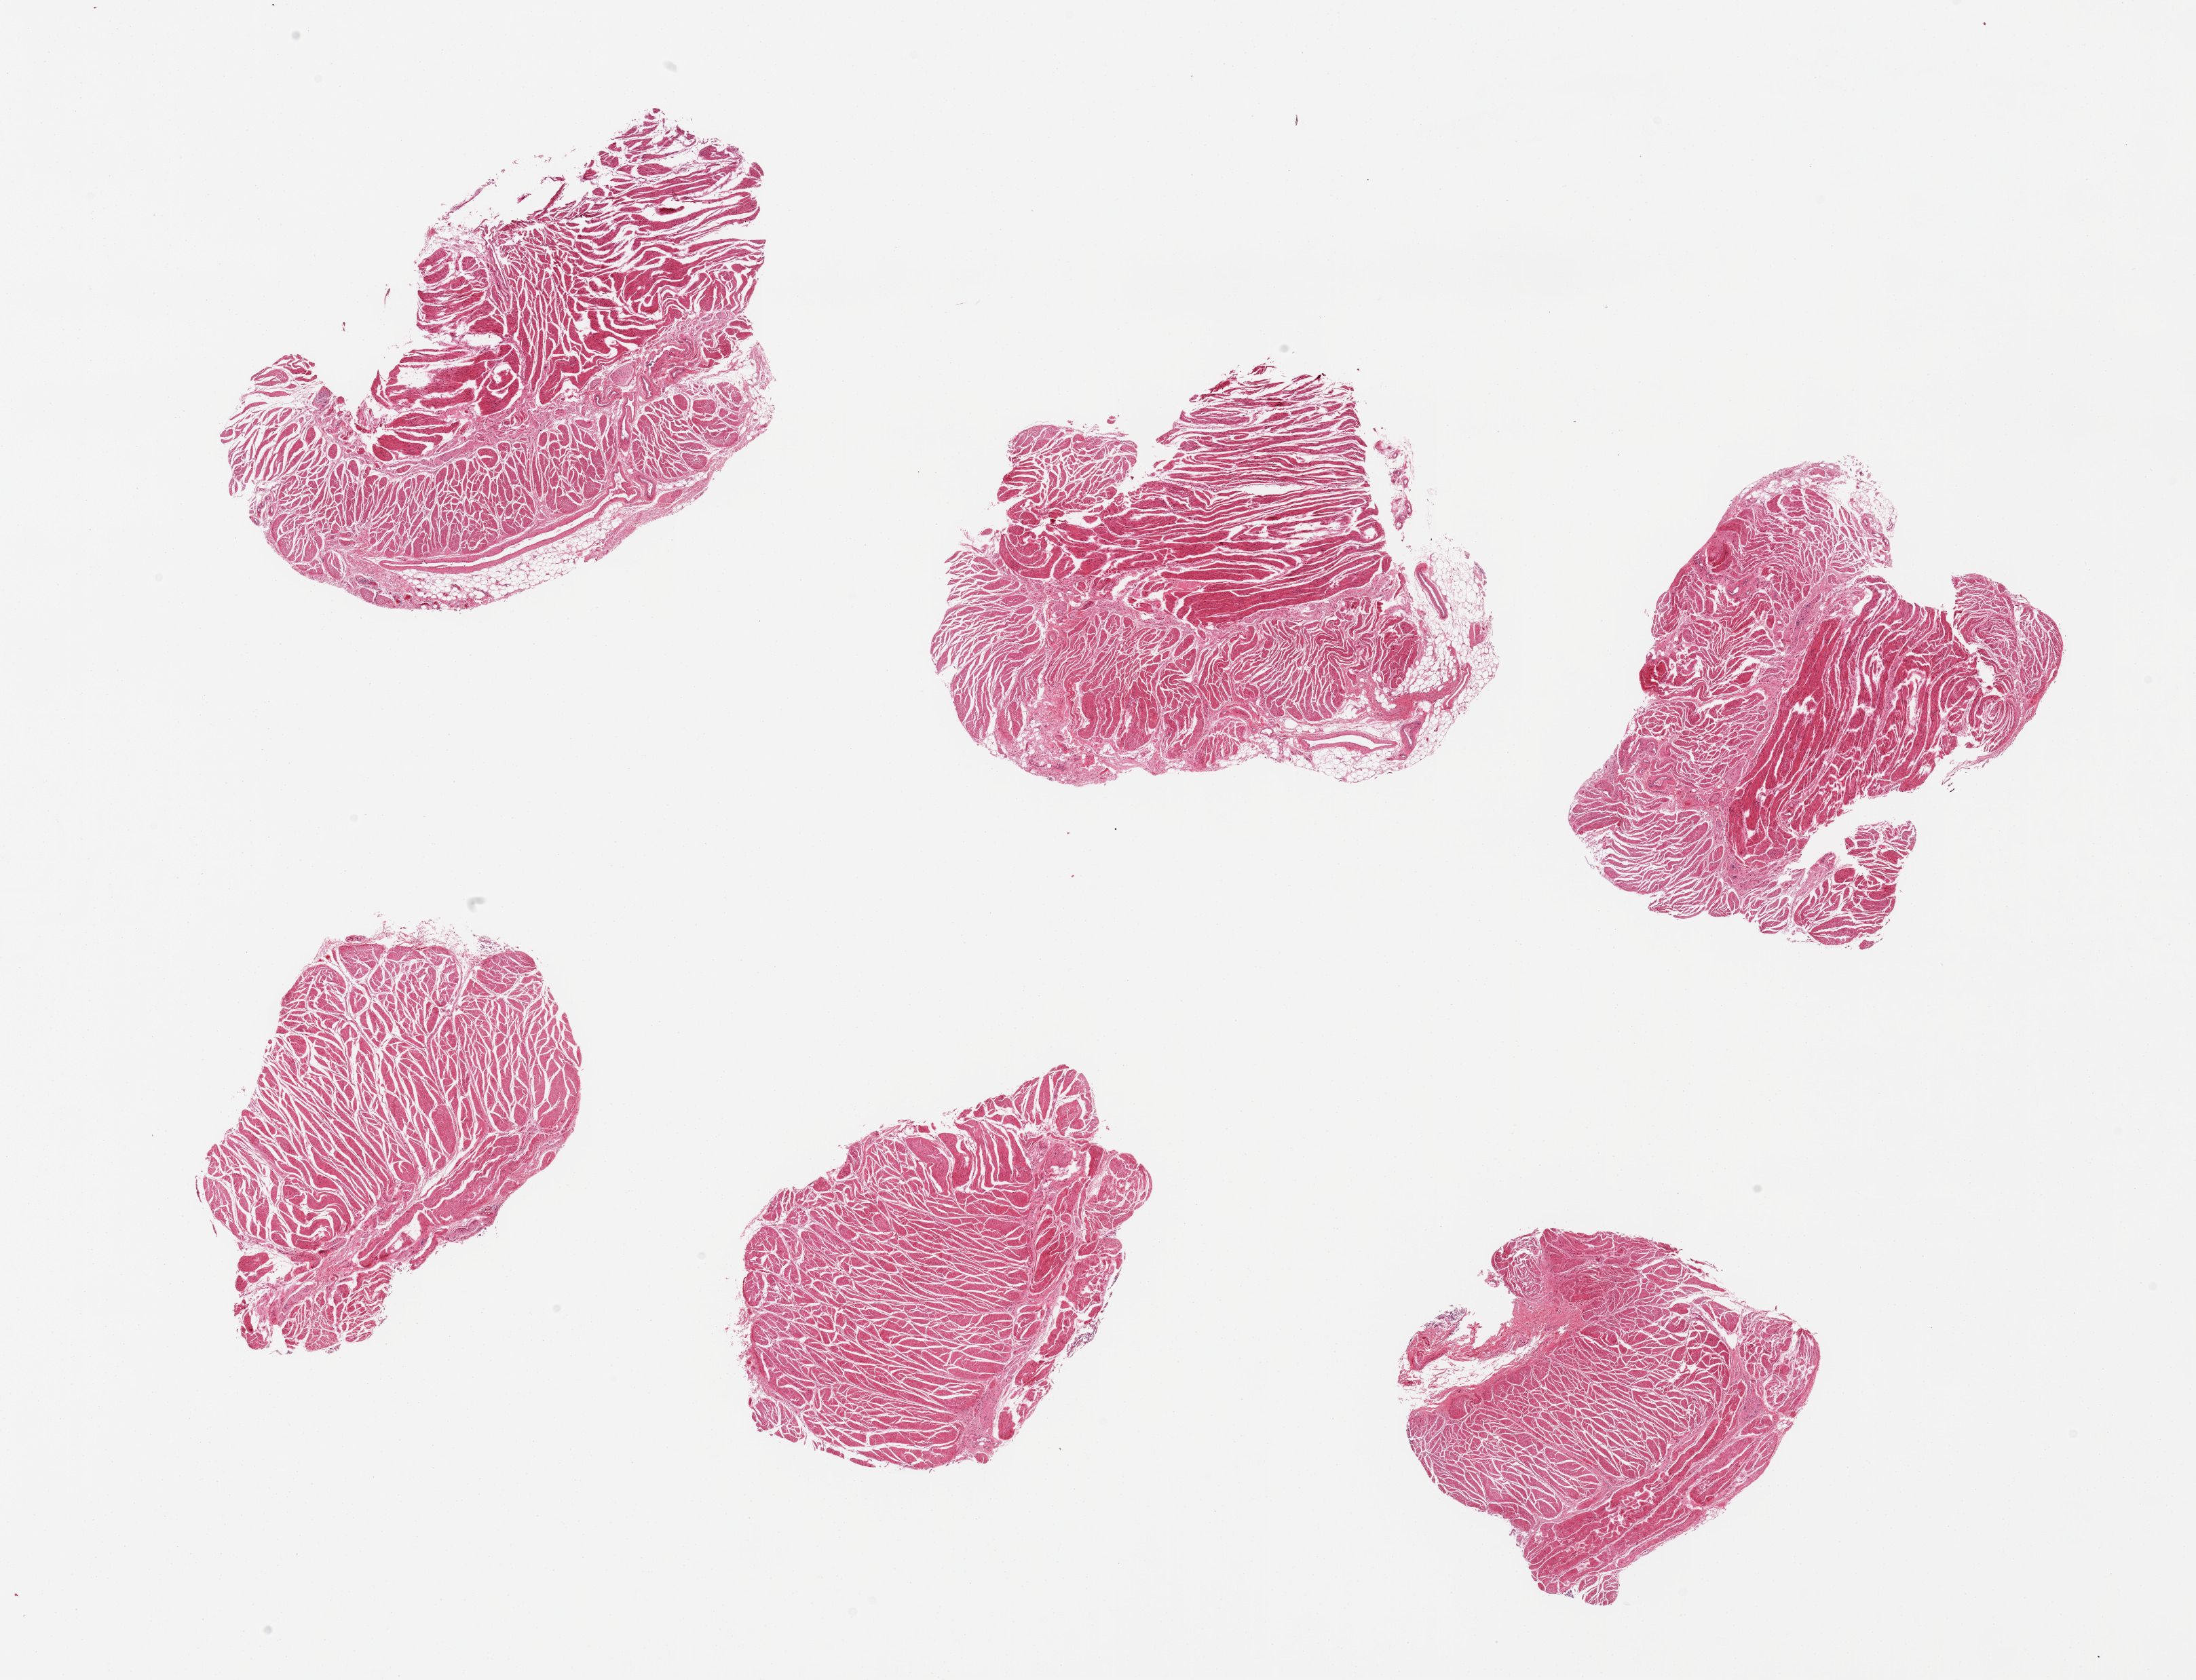
Haematoxylin and eosin whole-slide image, low-resolution overview of the scanned area, about 25.6 x 19.6 mm; PAXgene-fixed, paraffin-embedded tissue; sampled site (target tissue): gastroesophageal junction; donor tissue sample.
• reviewer comment on this tissue sample: 6 pieces, all muscularis